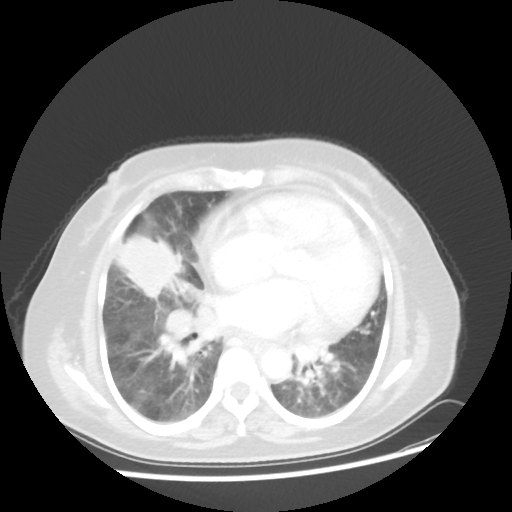
Chest CT, one axial slice. Position 20 of 45 along the scan axis. Reconstruction kernel STANDARD. Lung window (W 1500 / L -600 HU). 5 mm slice thickness. 512 × 512 image matrix. Patient: female, 67 years. Case-level facts recorded for this patient, not image findings: clinical TNM (as recorded): T2a N3 M1a.
Annotated regions visible in this slice (bounding box drawn by a radiologist):
- lung tumour (recorded histology: adenocarcinoma): box from (x=121, y=230) to (x=186, y=306) px